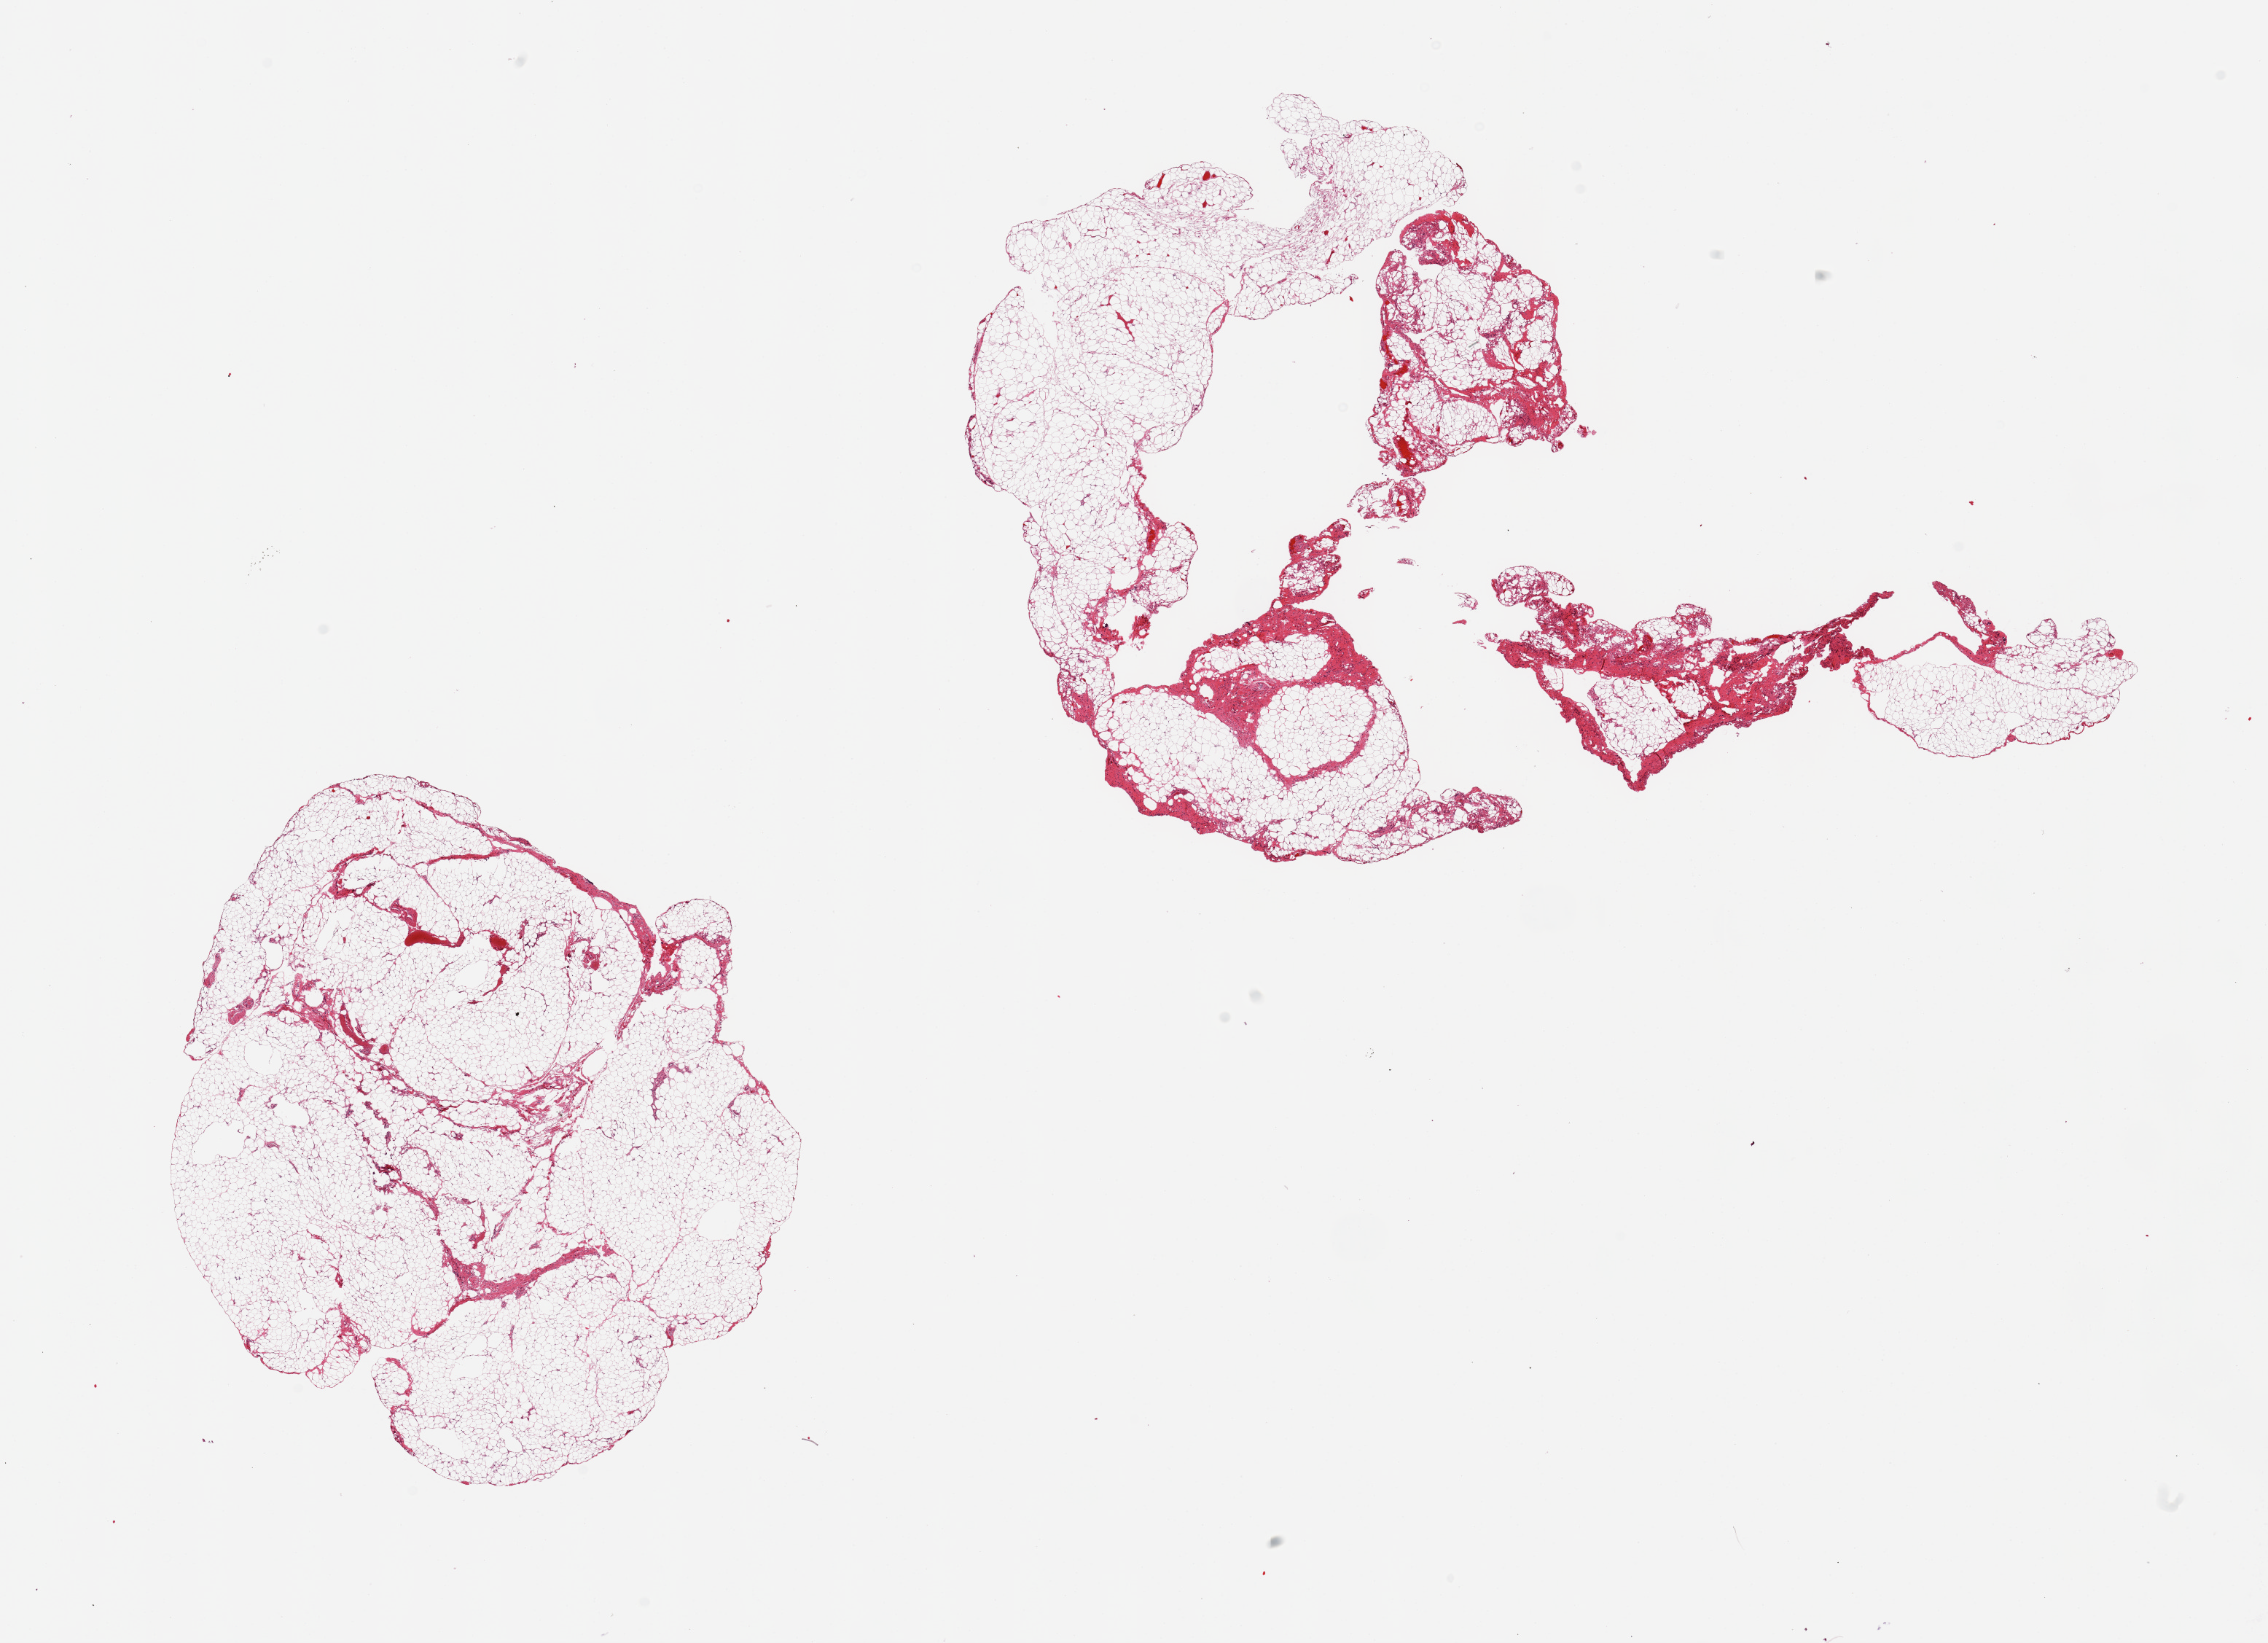
Whole-slide image, H&E stain, brightfield — shown as a low-resolution overview of the whole scanned area (about 24.6 x 17.8 mm, slide scanned at 20x); PAXgene-fixed, paraffin-embedded tissue; section of omentum (target tissue); donor tissue sample. Donor: male.
Pathologist's review note for this sample: 2 pieces; ~10% fibrovascular component.